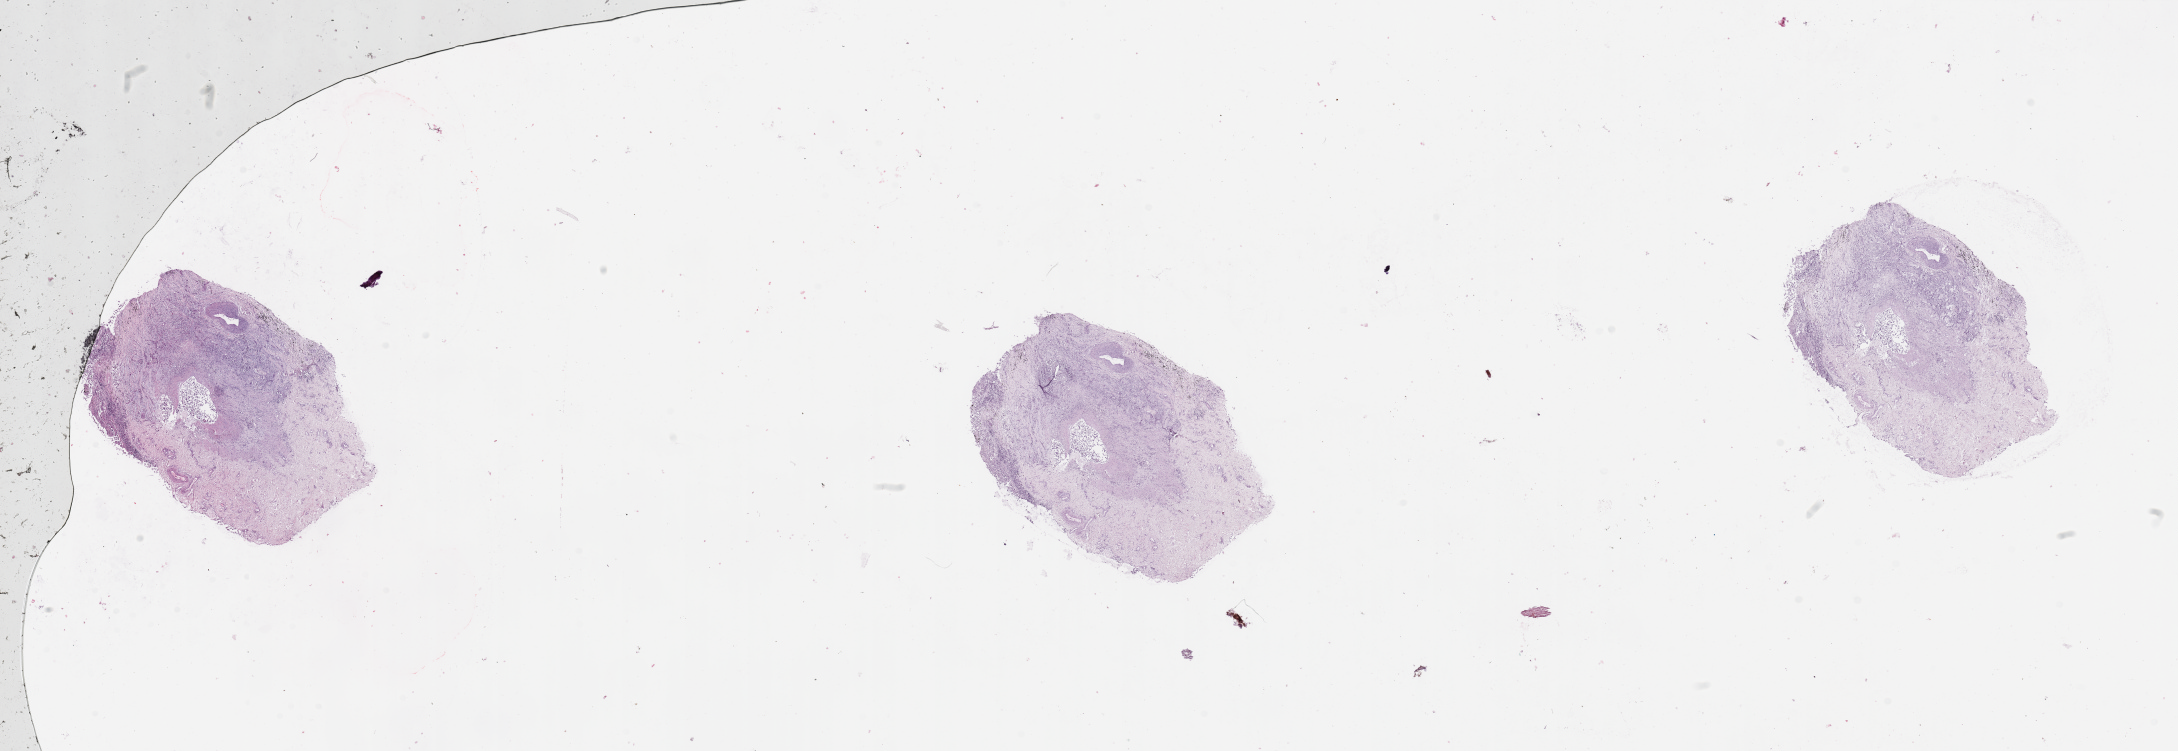
Whole-slide histology image, H&E, low-resolution overview of the scanned area, about 34.5 x 11.9 mm; tumour tissue sample, lung. Male, 76 y/o. Histologic grade: G2 (moderately differentiated).
AJCC pathologic stage: IIA. Histologic diagnosis: Adenocarcinoma, NOS.